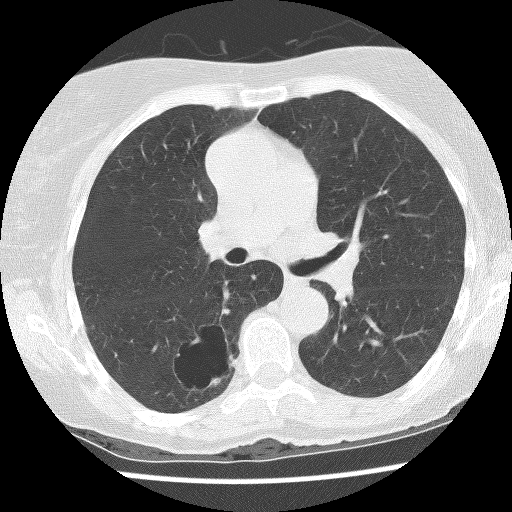
Low-dose screening chest CT, axial slice. Baseline annual screen. Lung window (W 1500 / L -600 HU). 2.5 mm slice thickness. Slice 53 of 136 in the series. 512 × 512 image matrix, field of view 300 × 300 mm. Female participant, aged 69 years at enrolment. Former smoker at enrolment.
Expert-annotated lung lesion, bounding box (x1, y1, x2, y2) in pixels: (158, 320, 247, 395). The screening reader recorded 2 non-calcified nodules or masses ≥4 mm on this exam (right lower lobe, right lower lobe); which of them this box marks is not recorded. Later outcome: lung cancer diagnosed 288 days after this screen — non-small cell carcinoma, right lower lobe, poorly differentiated (G3), stage IB (AJCC 6th edition), 36 mm at pathology.